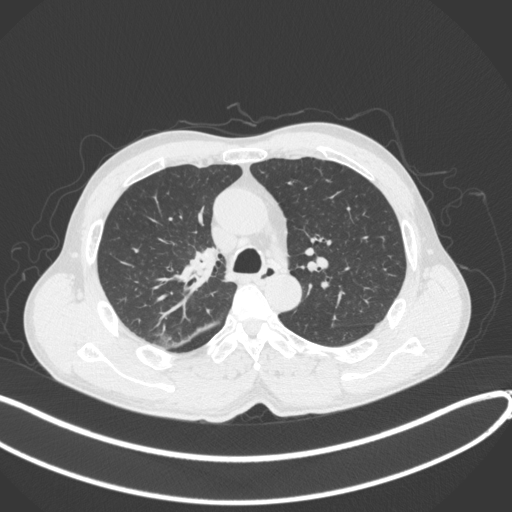
Chest CT, one axial slice. Position 264 of 409 along the scan axis. Reconstruction kernel B31f. 120 kVp. Lung window (W 1500 / L -600 HU). 512 × 512 image matrix. Male patient, age 53 years. Case-level facts recorded for this patient, not image findings: clinical TNM (as recorded): T1b N0 M0.
Outlined on this slice (rectangle marked by the reading radiologist):
- lung tumour (recorded histology: squamous cell carcinoma): bounding box (x1, y1, x2, y2) in pixels: (183, 247, 224, 284)